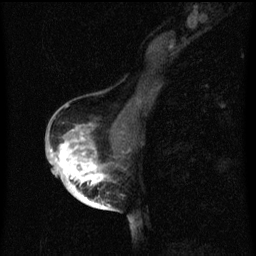
Breast MRI (dynamic contrast-enhanced), one sagittal slice; dynamic contrast-enhanced series, image 2 of 3 at this slice position (ordered by acquisition); 1.5 T; TE 4.2 ms, TR 8 ms; 2 mm slice thickness; 256 × 256 image matrix, field of view 180 × 180 mm. Female patient, age 56 years.
Structures marked on this image (semi-automatic segmentation, software-assisted and operator-edited):
- analysis volume of interest (the breast-tissue region the enhancement analysis was run in; not a lesion): bounding box [x1, y1, x2, y2] px = [54, 126, 120, 199]
- tumour enhancement mask (voxels above the 70 % enhancement threshold inside the analysis volume of interest): [55, 126, 107, 199]